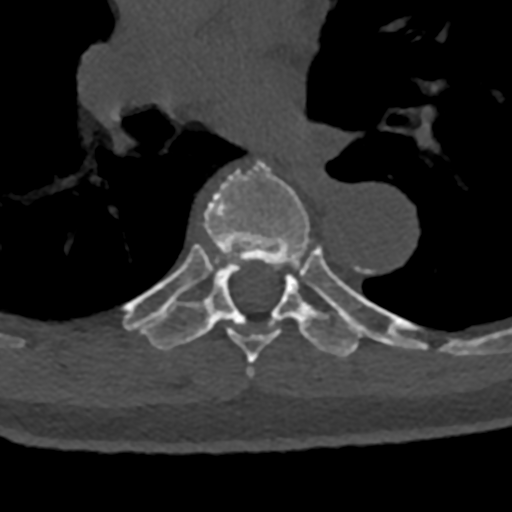
CT including the spine, one axial slice; slice 785 of 797 in the series (ordered by position); reconstruction kernel Br40s/3; 120 kVp; bone window (W 1800 / L 400 HU); 512 × 512 image matrix, field of view 160 × 160 mm. Patient: male, 74 years. Case-level facts recorded for this patient, not image findings: primary cancer: renal; vertebrae with lytic lesions (as recorded): T10, L1, L2, L3, L4, L5.
Annotated regions visible in this slice (semi-automatically segmented with operator editing):
- T6 vertebra: bounding box (x1, y1, x2, y2) in pixels: (167, 160, 310, 377)
- T7 vertebra: (124, 246, 428, 358)